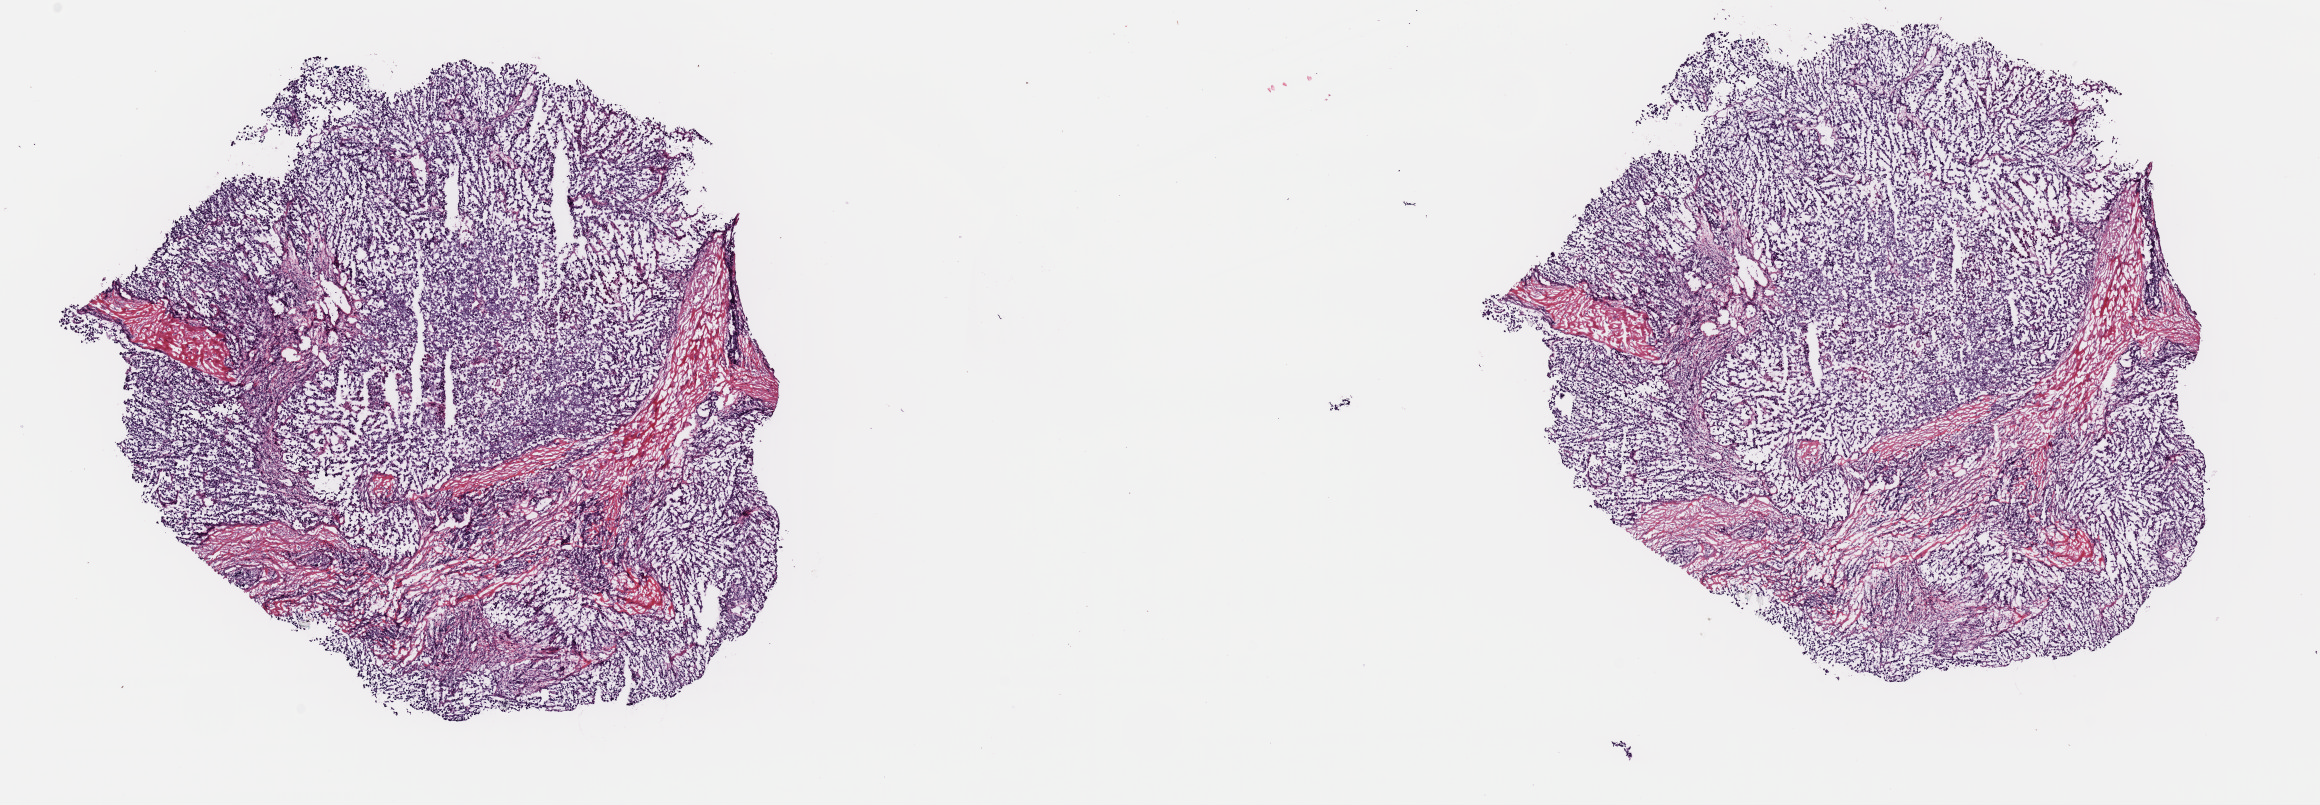
Digitized H&E-stained tissue section (whole slide), shown as a low-resolution overview of the whole scanned area (about 18.3 x 6.4 mm, from a 40x scan); frozen section; metastatic tumour sample, sampled site: lymph nodes of axilla or arm. Male patient; age at initial diagnosis 44 years. Composition of this section per pathologist review: tumour cells 95%, tumour nuclei 95%, normal cells 0%, stromal cells 5%, necrosis 0%. Inflammatory infiltration, as recorded: lymphocyte infiltration 0%, monocyte infiltration 0%, neutrophil infiltration 0%.
This section: metastatic tumour tissue. Patient diagnosis: Amelanotic melanoma.